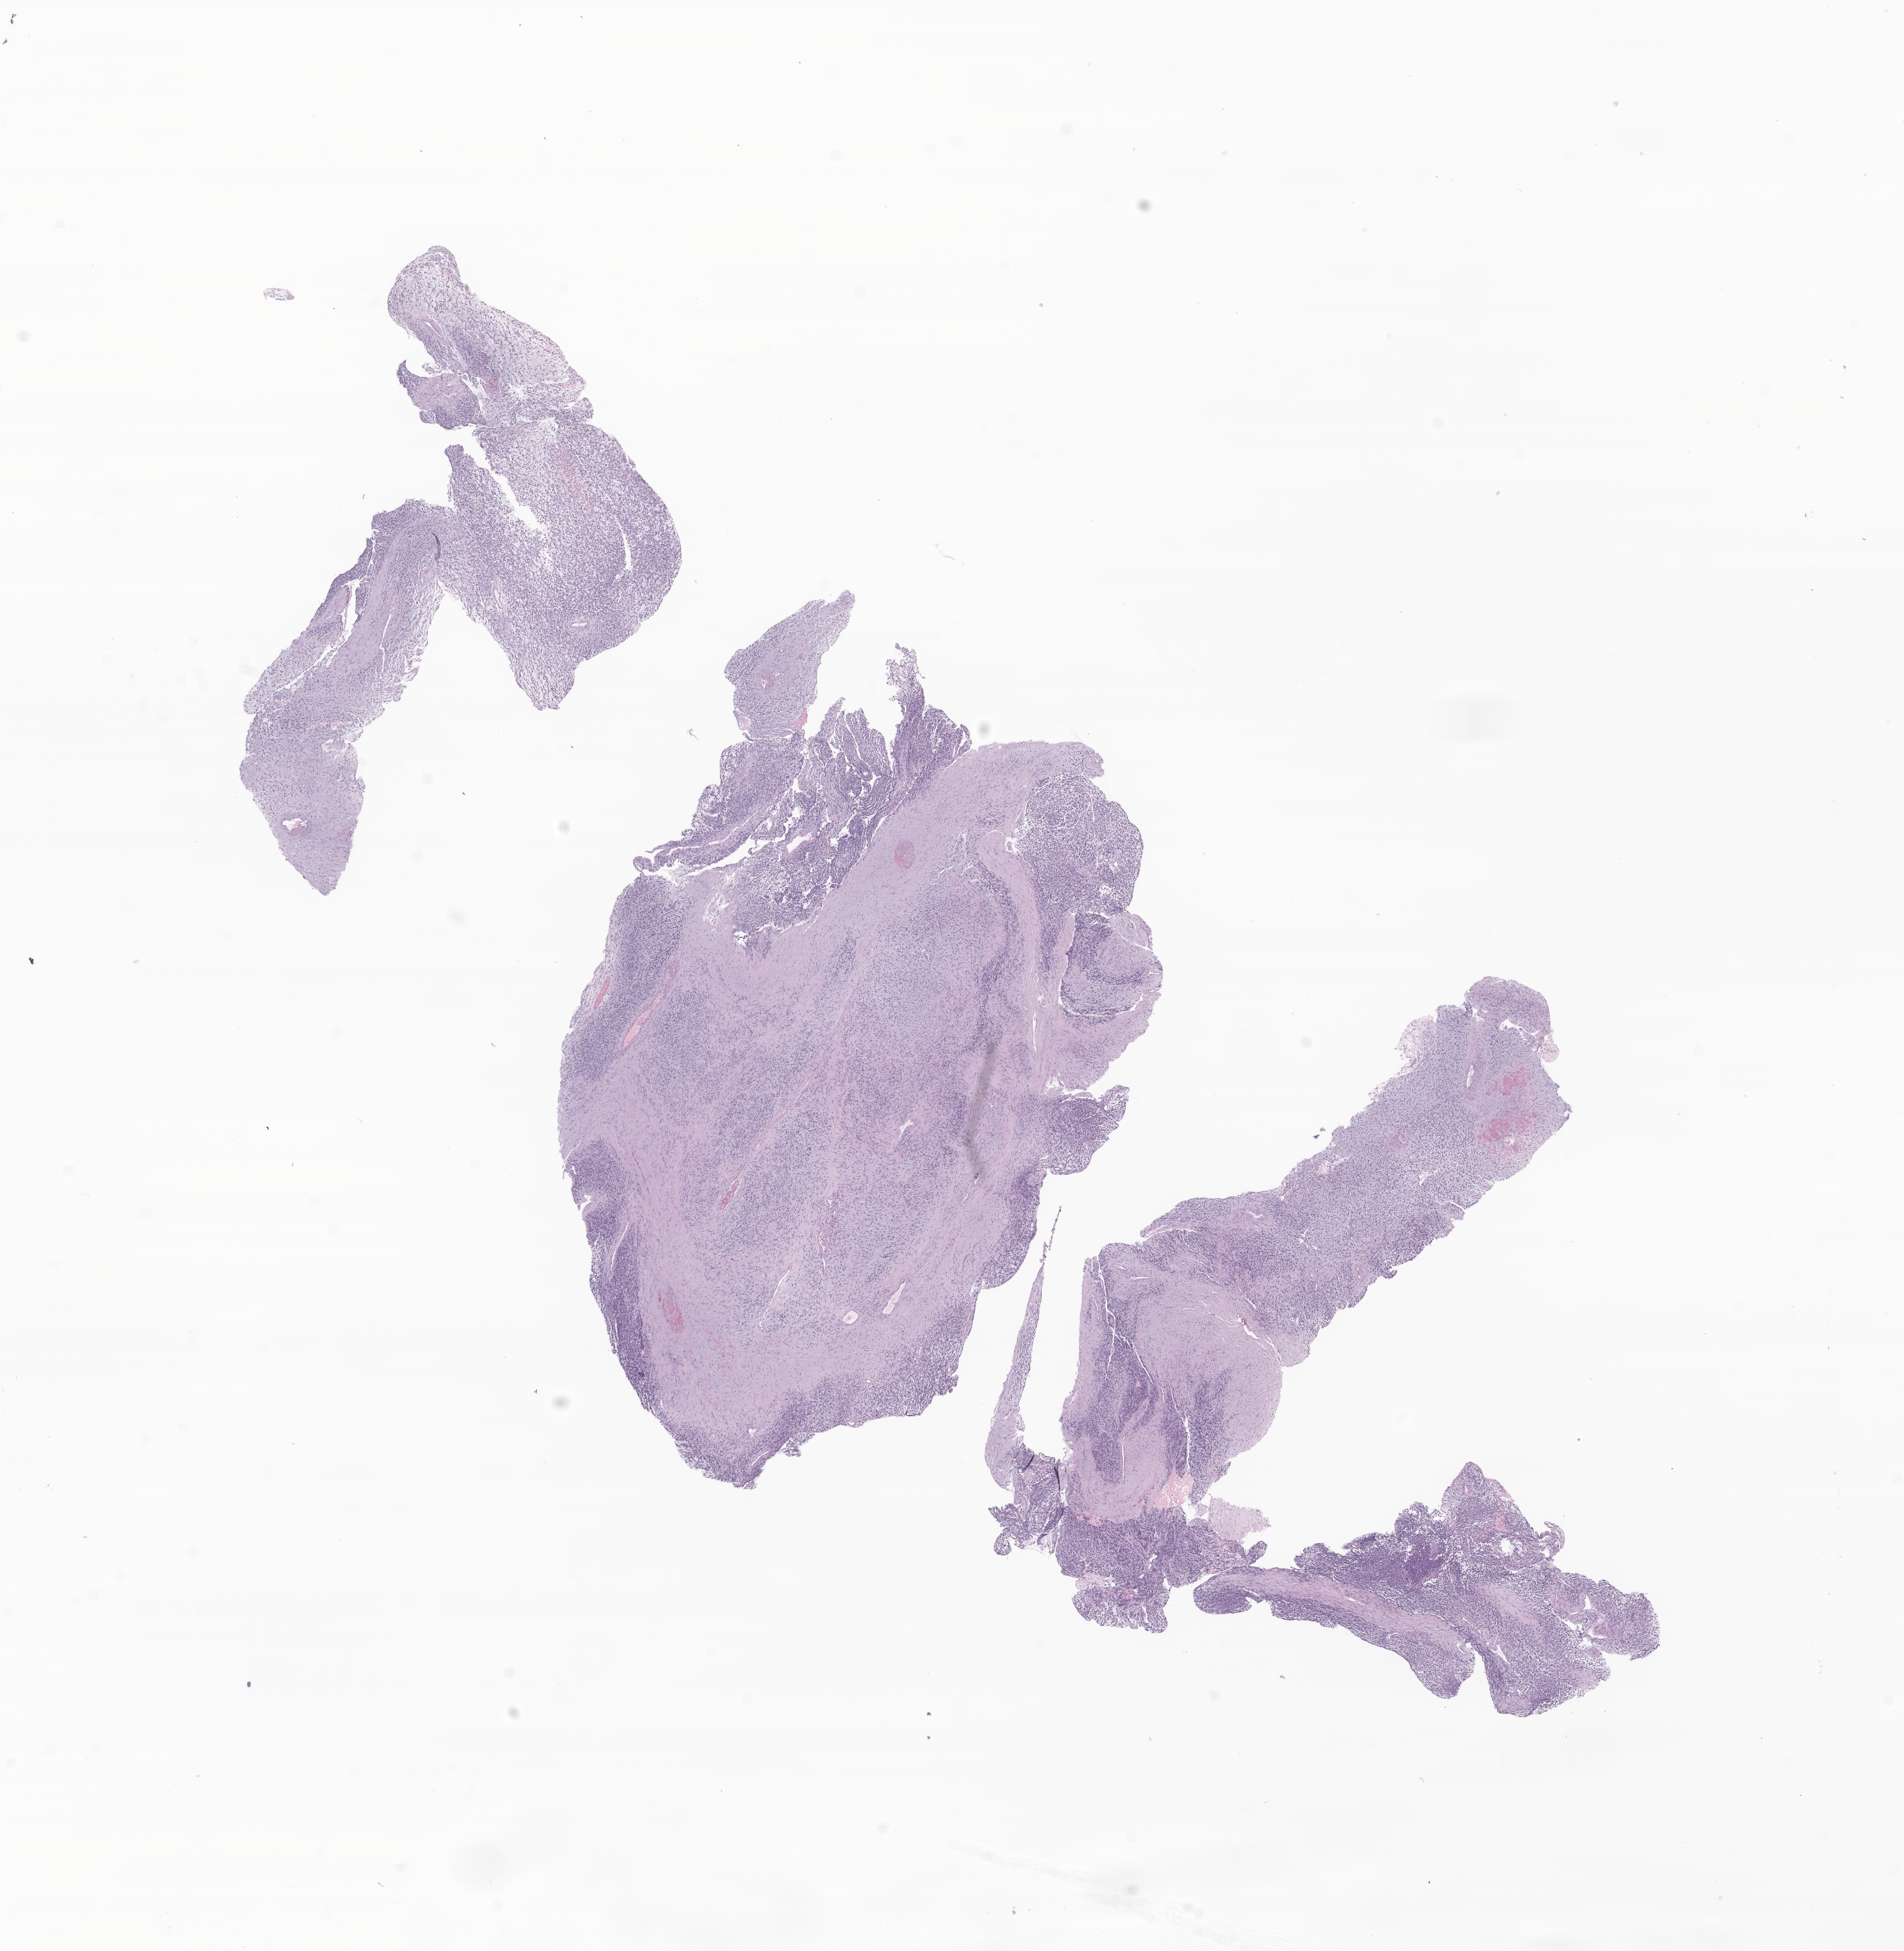
Hematoxylin and eosin (H&E) whole-slide image of tumor tissue from the gallbladder — whole scanned area (about 15.3 x 15.7 mm) shown as a low-resolution overview, formalin-fixed paraffin-embedded section. Patient female; age 62 months (5 years 2 months).
Diagnosis (ICD-O-3 morphology term): Rhabdomyosarcoma, NOS.